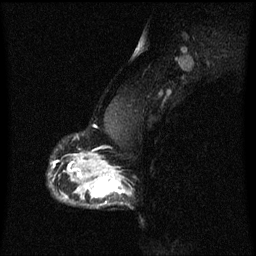
Breast MRI (dynamic contrast-enhanced), one sagittal slice. Position 43 of 60 along the scan axis. Dynamic contrast-enhanced series, image 2 of 3 at this slice position (ordered by acquisition). 1.5 T. TE 4.2 ms, TR 8.4 ms. 2 mm slice thickness. 256 × 256 image matrix. Patient: female, 40 years.
Outlined on this slice (semi-automatic segmentation, software-assisted and operator-edited):
- analysis volume of interest (the breast-tissue region the enhancement analysis was run in; not a lesion): bounding box <76,172,130,209> (left, top, right, bottom; pixels)
- tumour enhancement mask (voxels above the 70 % enhancement threshold inside the analysis volume of interest): <78,172,130,205>